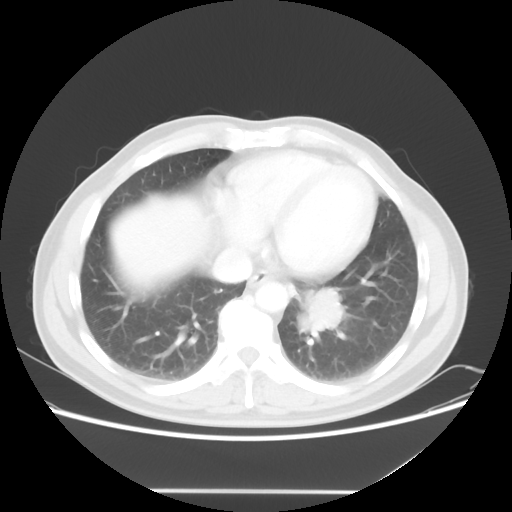
Chest CT, one axial slice; lung window (W 1500 / L -600 HU); 5 mm slice thickness; 512 × 512 image matrix, field of view 385 × 385 mm. Patient: male, 61 years. Case-level facts recorded for this patient, not image findings: clinical TNM (as recorded): T1c N0 M0; histopathological grade: G3.
Outlined on this slice (bounding box drawn by a radiologist):
- lung tumour (recorded histology: adenocarcinoma): bounding box [x1, y1, x2, y2] px = [294, 283, 356, 345]